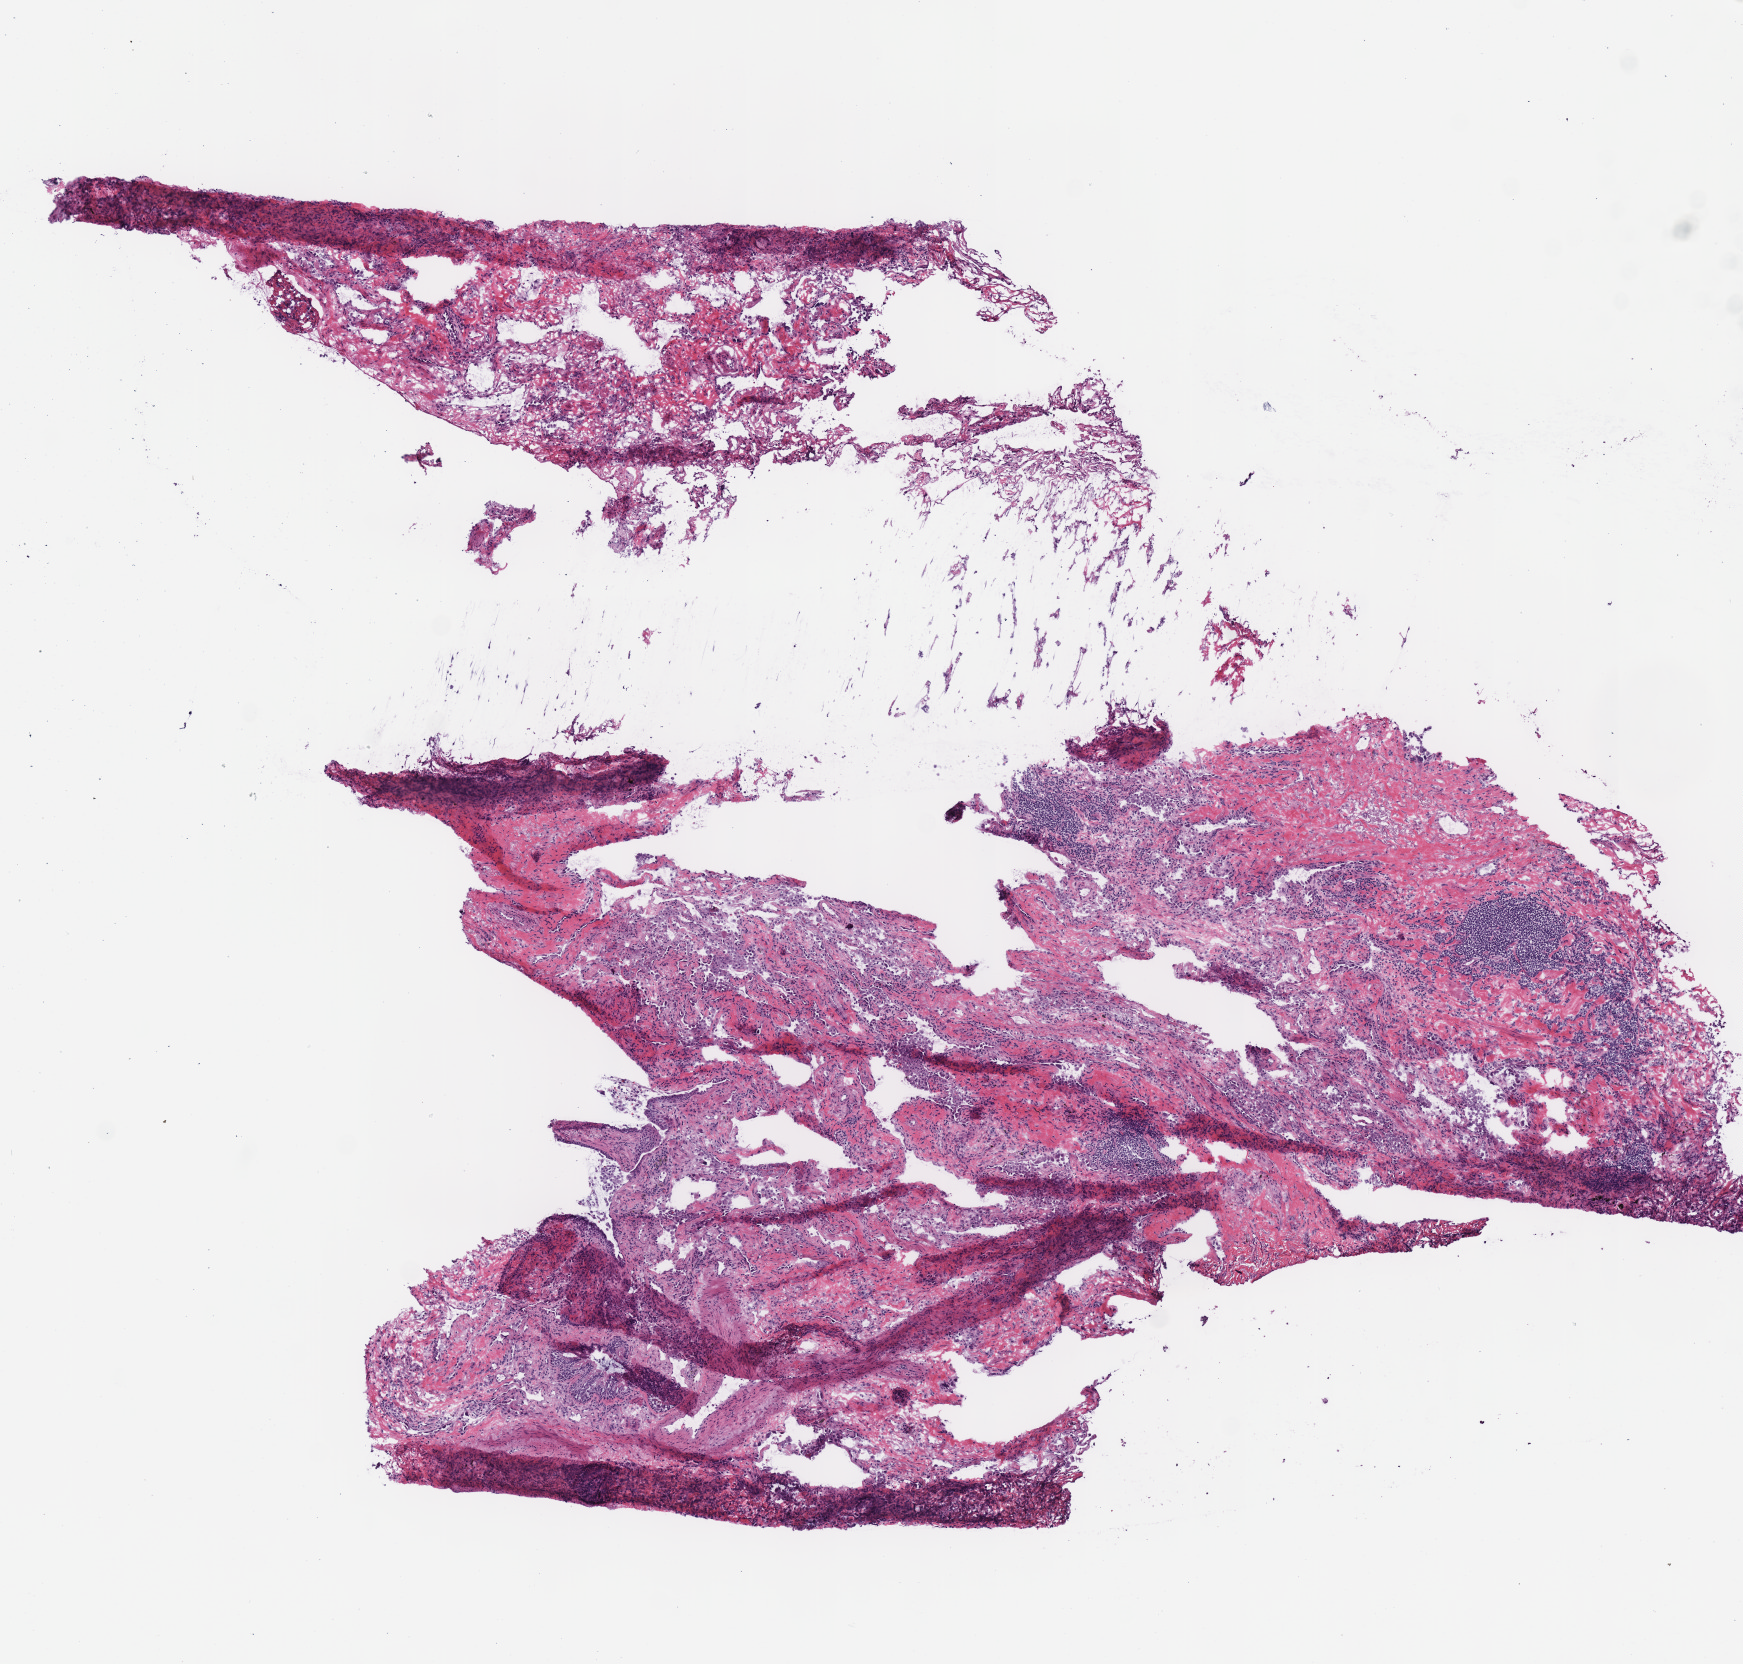
Whole-slide histology image, H&E-stained, shown as a low-resolution overview of the whole scanned area (about 6.9 x 6.5 mm, acquisition: 40x scan); frozen section from the top of the tissue portion; lung, solid tissue normal (non-tumour tissue) sample. Patient: female, age at initial diagnosis 68 years. Infiltration values recorded for this section: lymphocyte infiltration 20%, monocyte infiltration 10%, neutrophil infiltration 0%.
• this section: solid tissue normal (non-tumour) sample from the same patient
• patient diagnosis: Squamous cell carcinoma, NOS